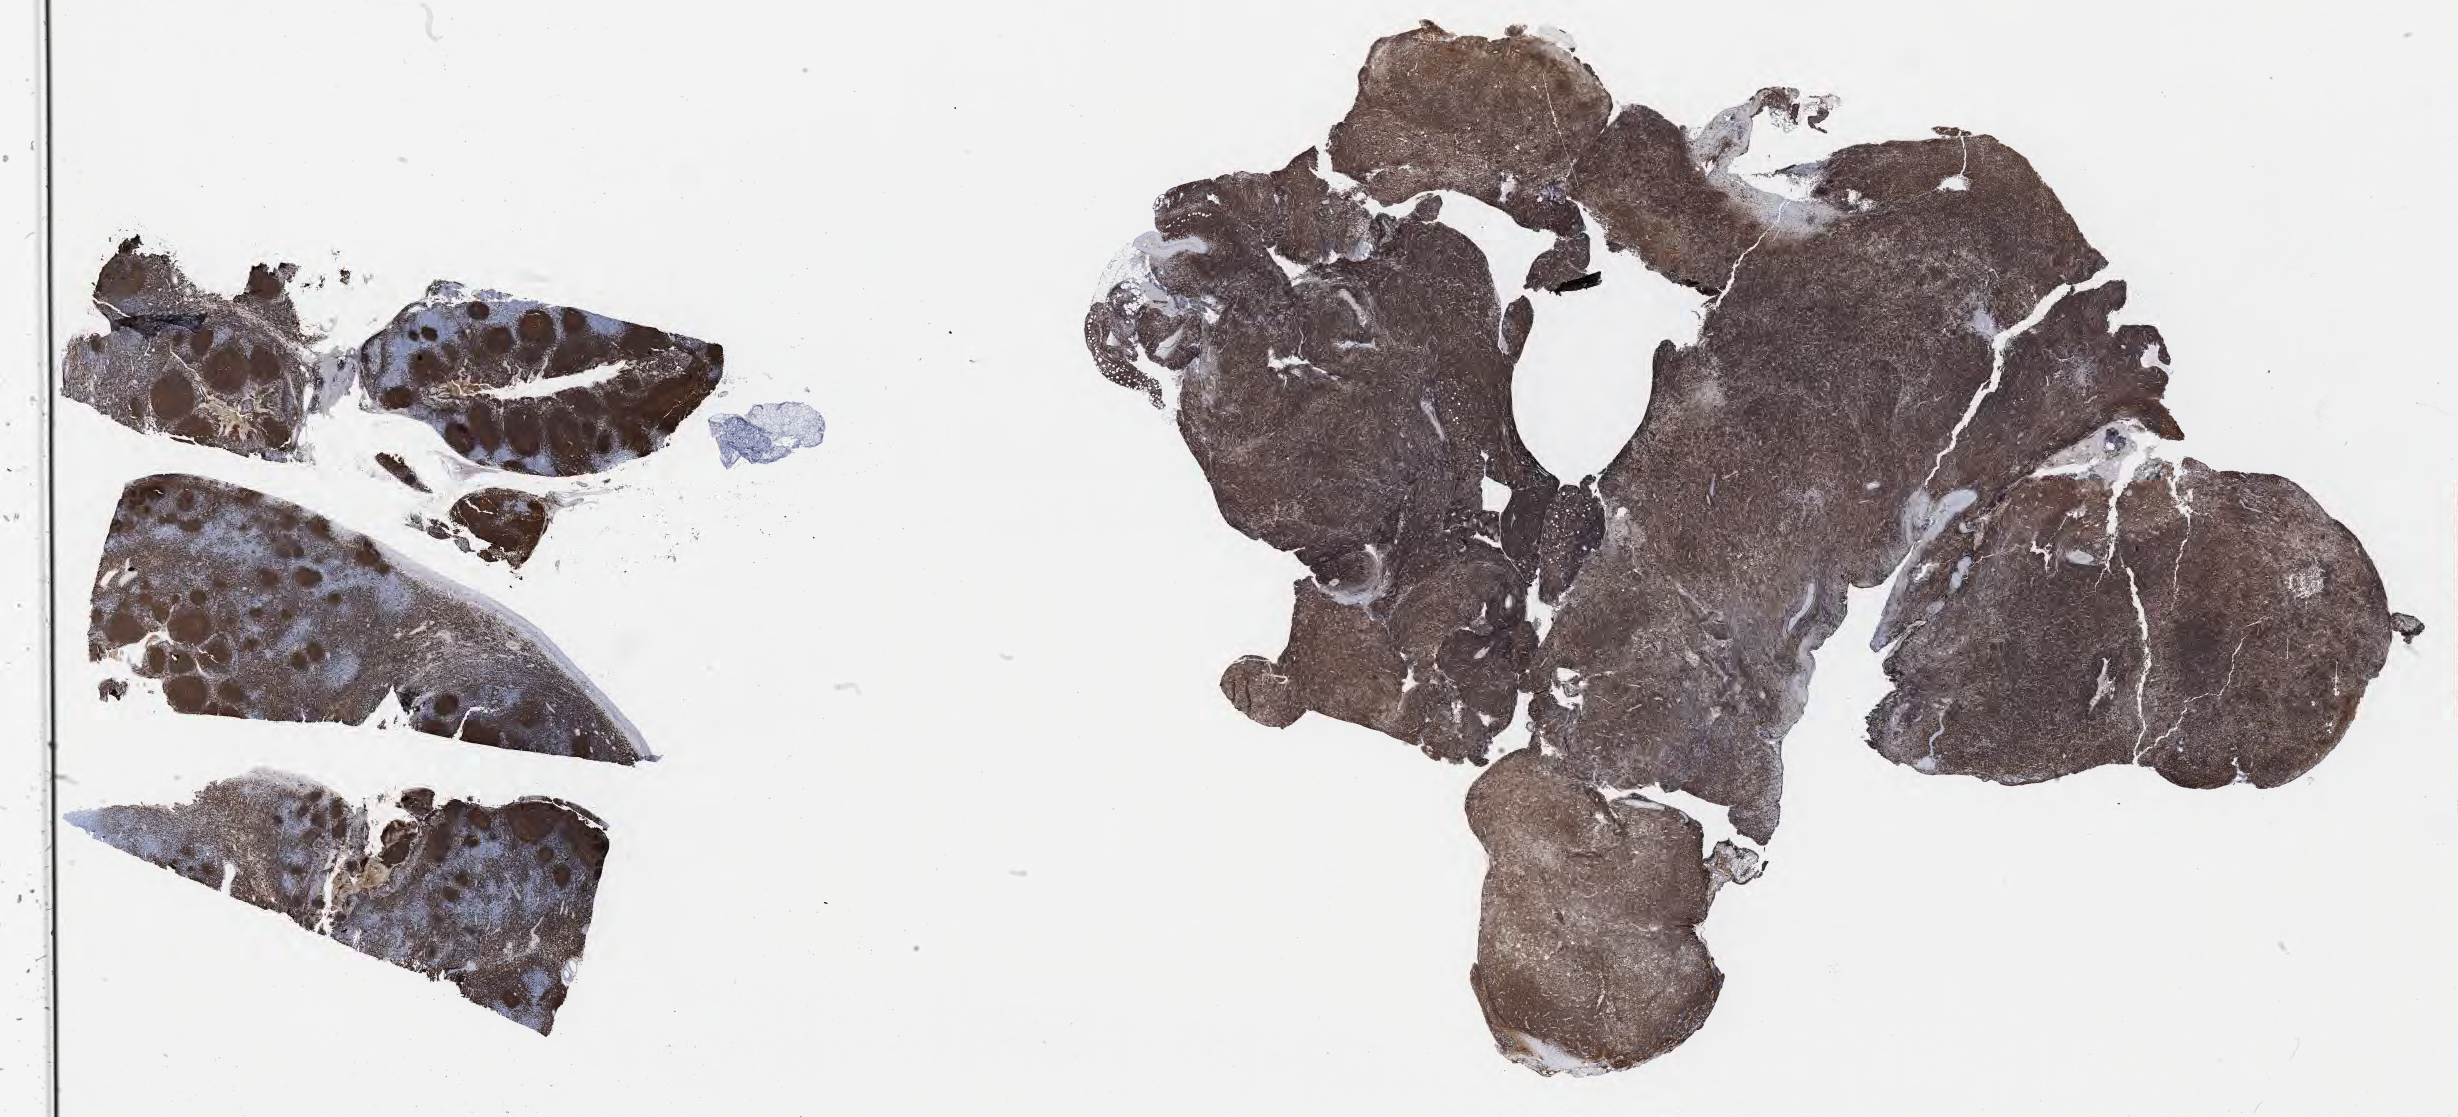
Whole-slide image, immunohistochemical stain for CD20, a low-resolution overview of the entire scanned area, about 39.8 x 18.1 mm. Tumor tissue. Anatomic site: soft tissue of abdomen. Female patient; age at initial diagnosis 8 years.
* diagnosis: Burkitt lymphoma, NOS